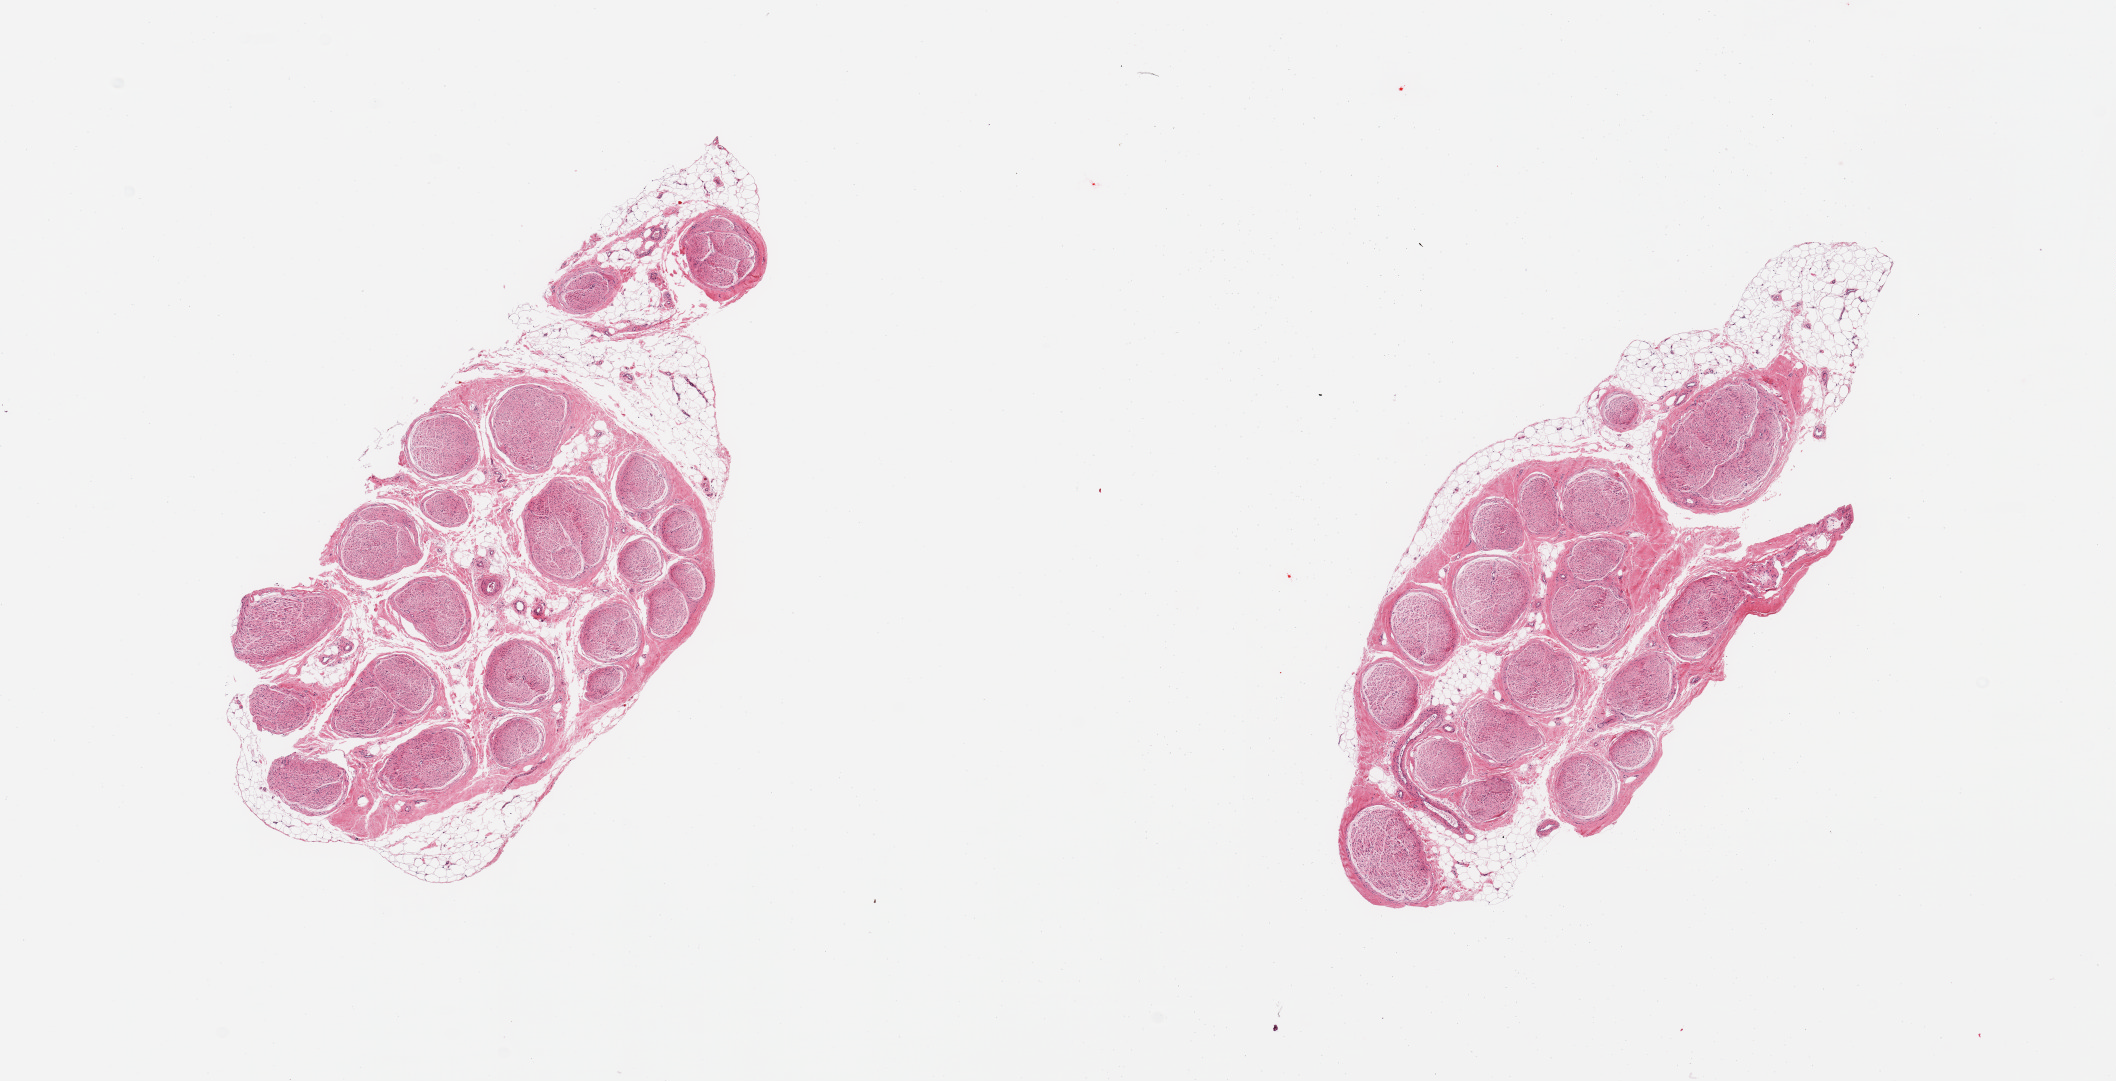
Hematoxylin and eosin (H&E) whole-slide image, a low-resolution overview of the entire scanned area, about 16.7 x 8.5 mm (slide scanned at 20x), PAXgene-fixed paraffin-embedded (PFPE) section, sampled site (target tissue): tibial nerve, donor tissue sample. Female donor.
Pathologist's review note for this sample: 2 pieces; 20% internal and external fat content.